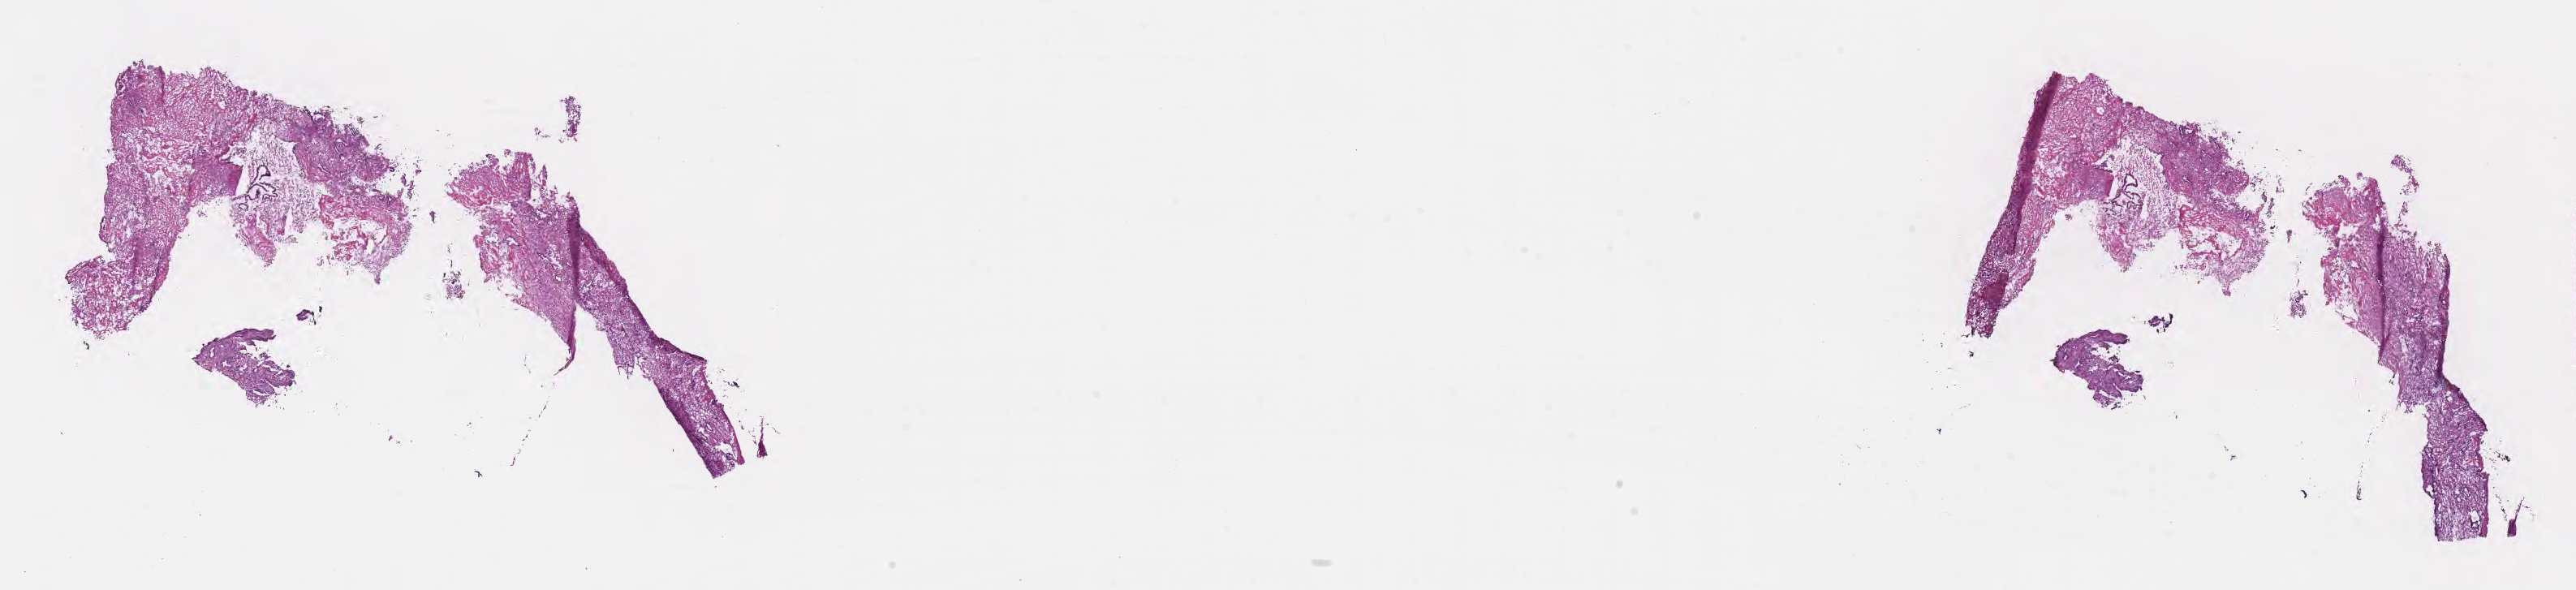
H&E whole-slide image — shown as a low-resolution overview of the whole scanned area (about 25.7 x 5.9 mm), frozen section, primary tumor, anatomic site: extrahepatic bile duct. Patient: male, age at initial diagnosis 52 years. Tumor grade: G2 (moderately differentiated). Pathologist review of this section (percent, as recorded): tumor cells 50%, tumor nuclei 50%, stromal cells 33%, necrosis 2%, normal cells 15%. Infiltration values recorded for this section: lymphocyte infiltration 8%, monocyte infiltration 7%, neutrophil infiltration 9%.
- AJCC pathologic stage: Stage IIIA
- diagnosis: Adenocarcinoma, NOS
- section: bottom of the tissue portion